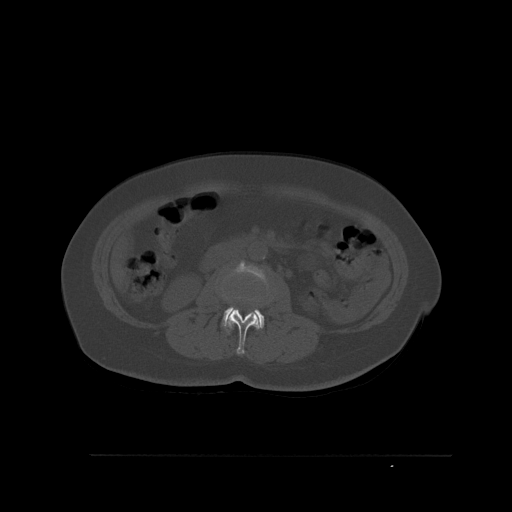
CT including the spine, one axial slice. Slice 238 of 527 in the series (ordered by position). Bone window (W 1800 / L 400 HU). 1.5 mm slice thickness. 512 × 512 image matrix. Female patient, age 73 years. From the clinical record (not read from this slice): primary cancer: breast; vertebrae with lytic lesions (as recorded): L2.
Annotated regions visible in this slice (semi-automatically segmented with operator editing):
- L2 vertebra: bounding box (x1, y1, x2, y2) in pixels: (224, 295, 259, 354)
- L3 vertebra: (222, 263, 267, 333)
- L4 vertebra: (249, 312, 260, 329)